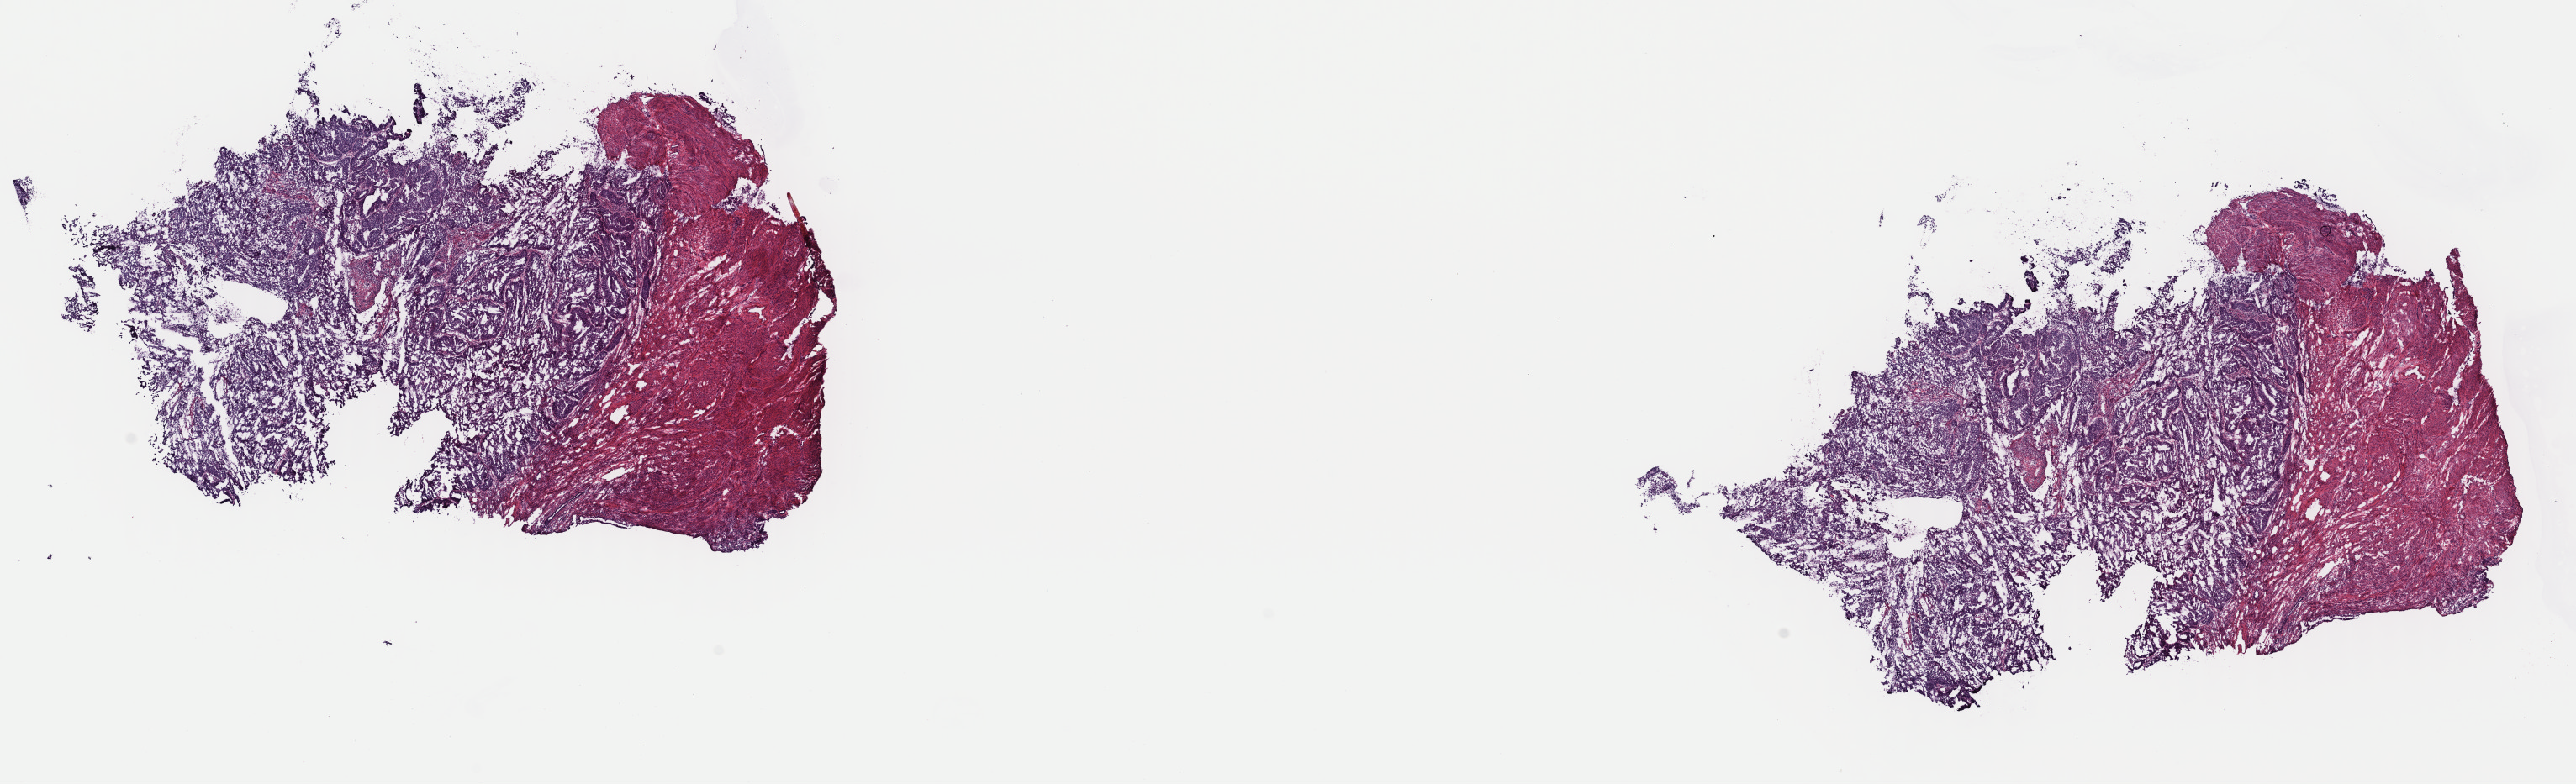
Digitized H&E tissue section (whole slide) — low-resolution overview of the scanned area, about 24.2 x 7.4 mm. Frozen section from the top of the tissue portion. Sample: primary tumour, uterus. Patient: female, age at initial diagnosis 61 years. Histologic grade: G2 (moderately differentiated). Slide review estimates, as recorded: tumour cells 70%, tumour nuclei 70%, normal cells 20%, stromal cells 10%, necrosis 0%. Infiltration values recorded for this section: lymphocyte infiltration 1%, monocyte infiltration 1%, neutrophil infiltration 1%.
Lymph nodes positive (case pathology): 0 of 28 examined. FIGO stage: IB. Histologic diagnosis: Endometrioid adenocarcinoma, NOS (endometrium).